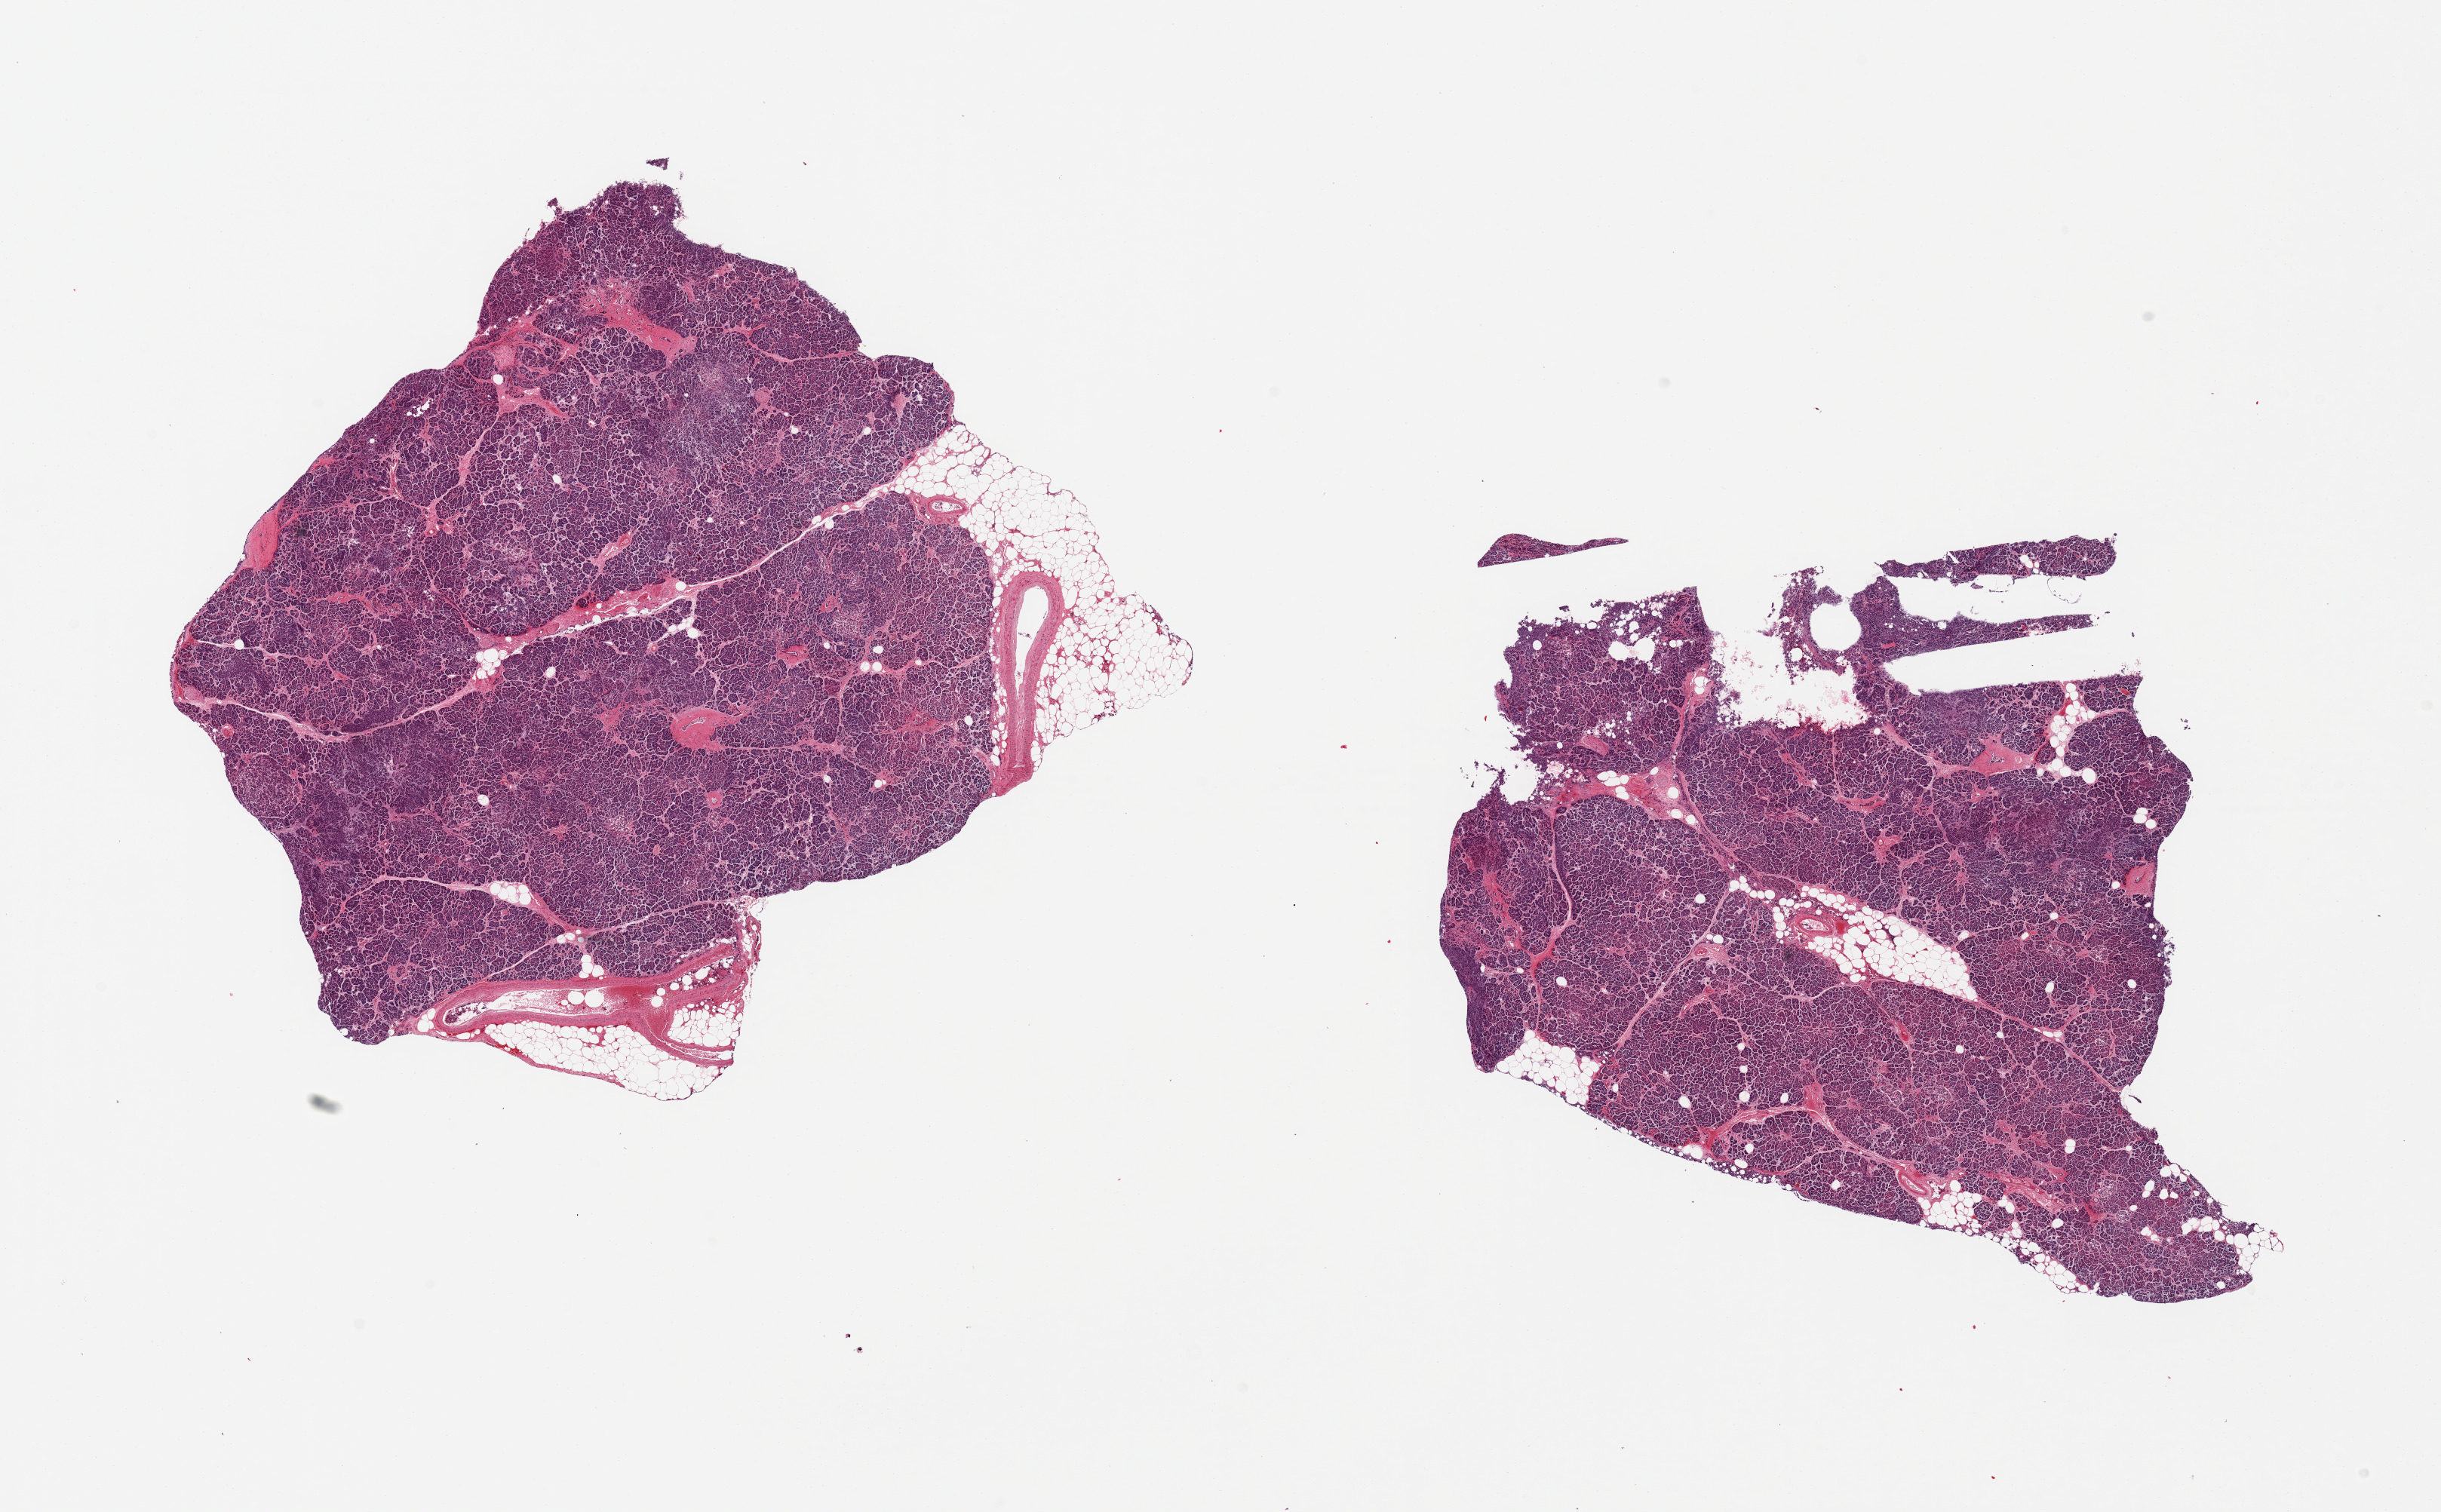
Digitized hematoxylin and eosin (H&E)-stained section, brightfield — a low-resolution overview of the entire scanned area, about 25.6 x 15.9 mm (acquisition: 20x scan). PAXgene-fixed, paraffin-embedded tissue. Target tissue: pancreas. Donor tissue sample. Donor: male.
- reviewer comment on this tissue sample: 2 pieces, mocderate saponification//autolysis, focally adherent fat, ~1mm